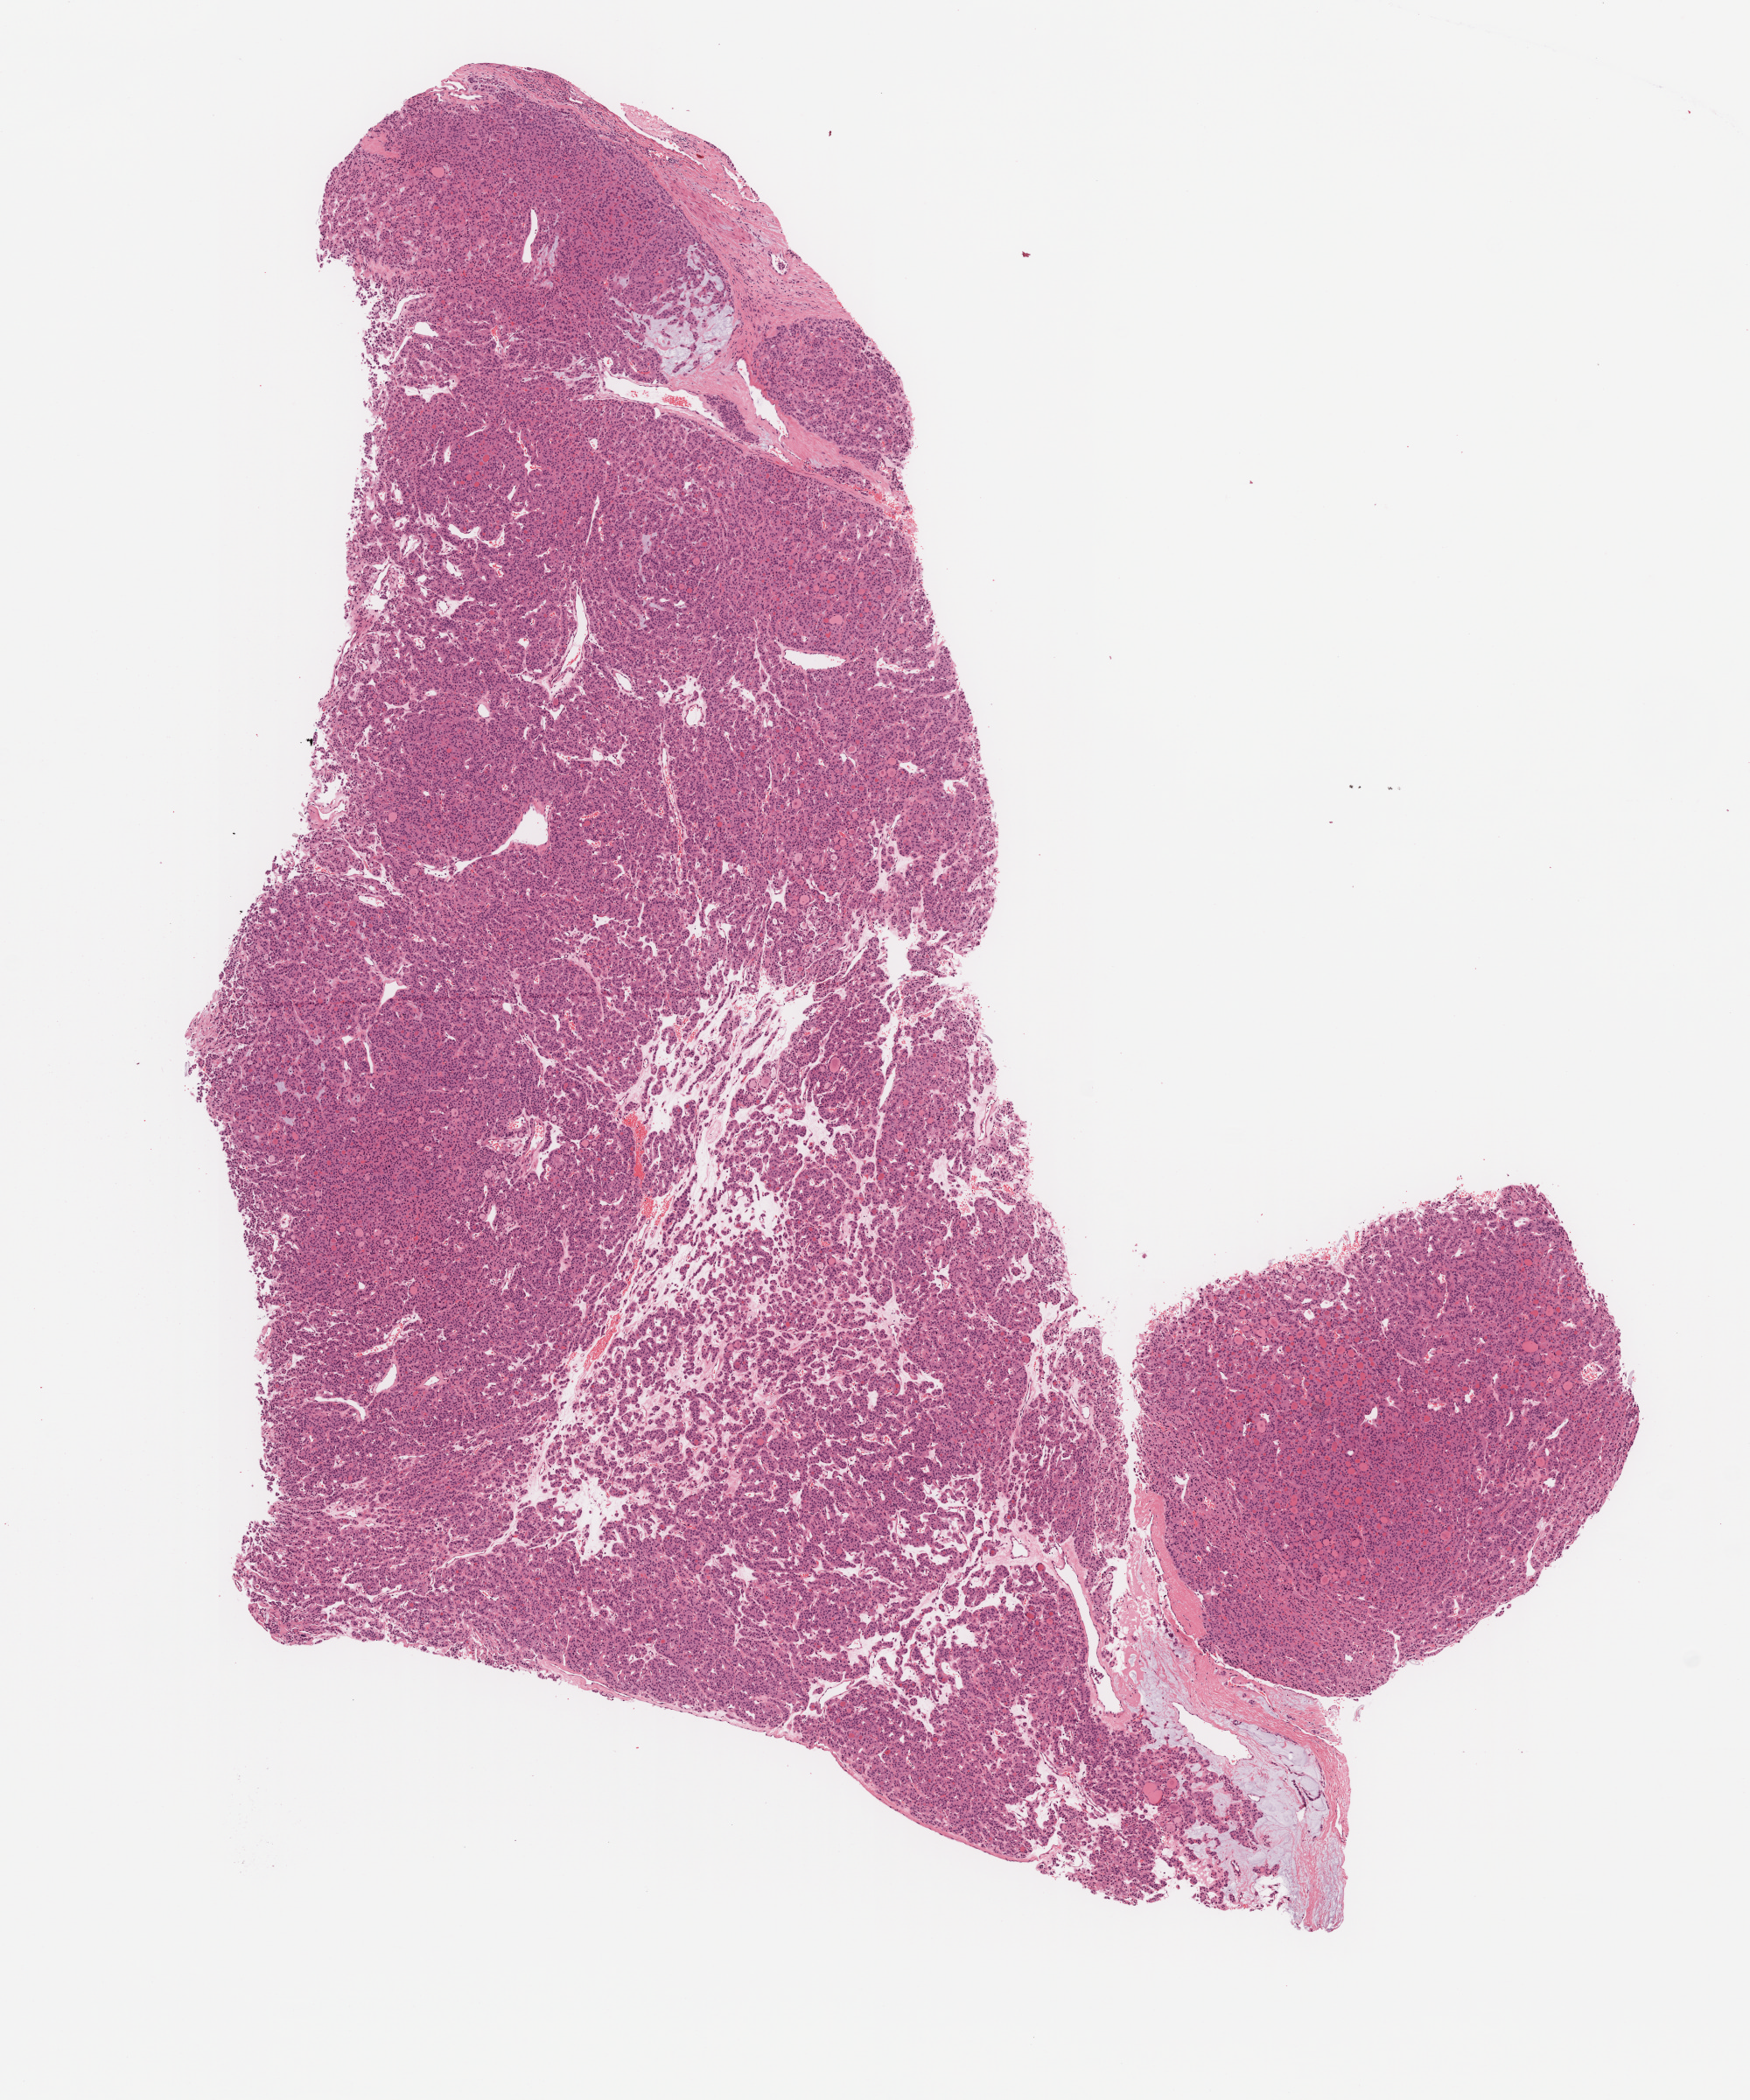
Whole-slide histology image, H&E-stained, whole scanned area (about 8.0 x 9.6 mm, from a 20x scan) shown as a low-resolution overview. Formalin-fixed paraffin-embedded (FFPE) diagnostic section. Sample: primary tumour, thyroid. Female patient; age at initial diagnosis 55 years.
Diagnosis: Papillary carcinoma, follicular variant. Laterality: right. Lymph nodes positive (case pathology): 0 of 1 examined. AJCC pathologic stage: II (7th edition).